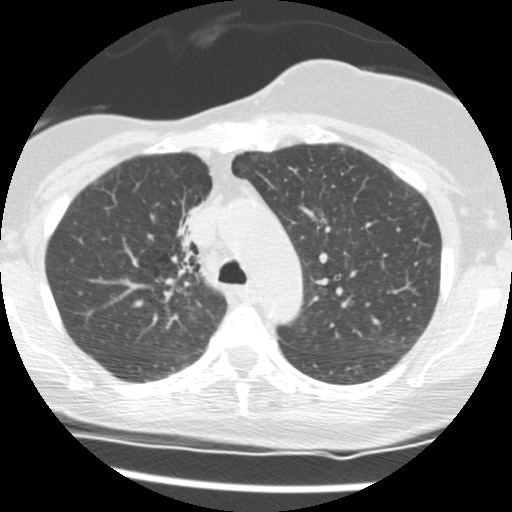
Chest CT (low-dose screening protocol), one axial image. Second screening round (one year after baseline). Lung window (W 1500 / L -600 HU). Female, age 56 years at enrolment.
Lesion marked by an expert reader, box from (x=154, y=197) to (x=213, y=276) px. The screening reader recorded 2 non-calcified nodules or masses ≥4 mm on this exam (right middle lobe, right lower lobe); which of them this box marks is not recorded. Official screen result: positive, change unspecified: nodule(s) >= 4 mm or enlarging nodule(s), mass(es), or other non-specific abnormalities suspicious for lung cancer. Later outcome: lung cancer diagnosed 675 days after this screen (after the third annual screen) — adenocarcinoma, NOS, right upper lobe, stage IIIB (AJCC 6th edition), 8 mm at pathology.